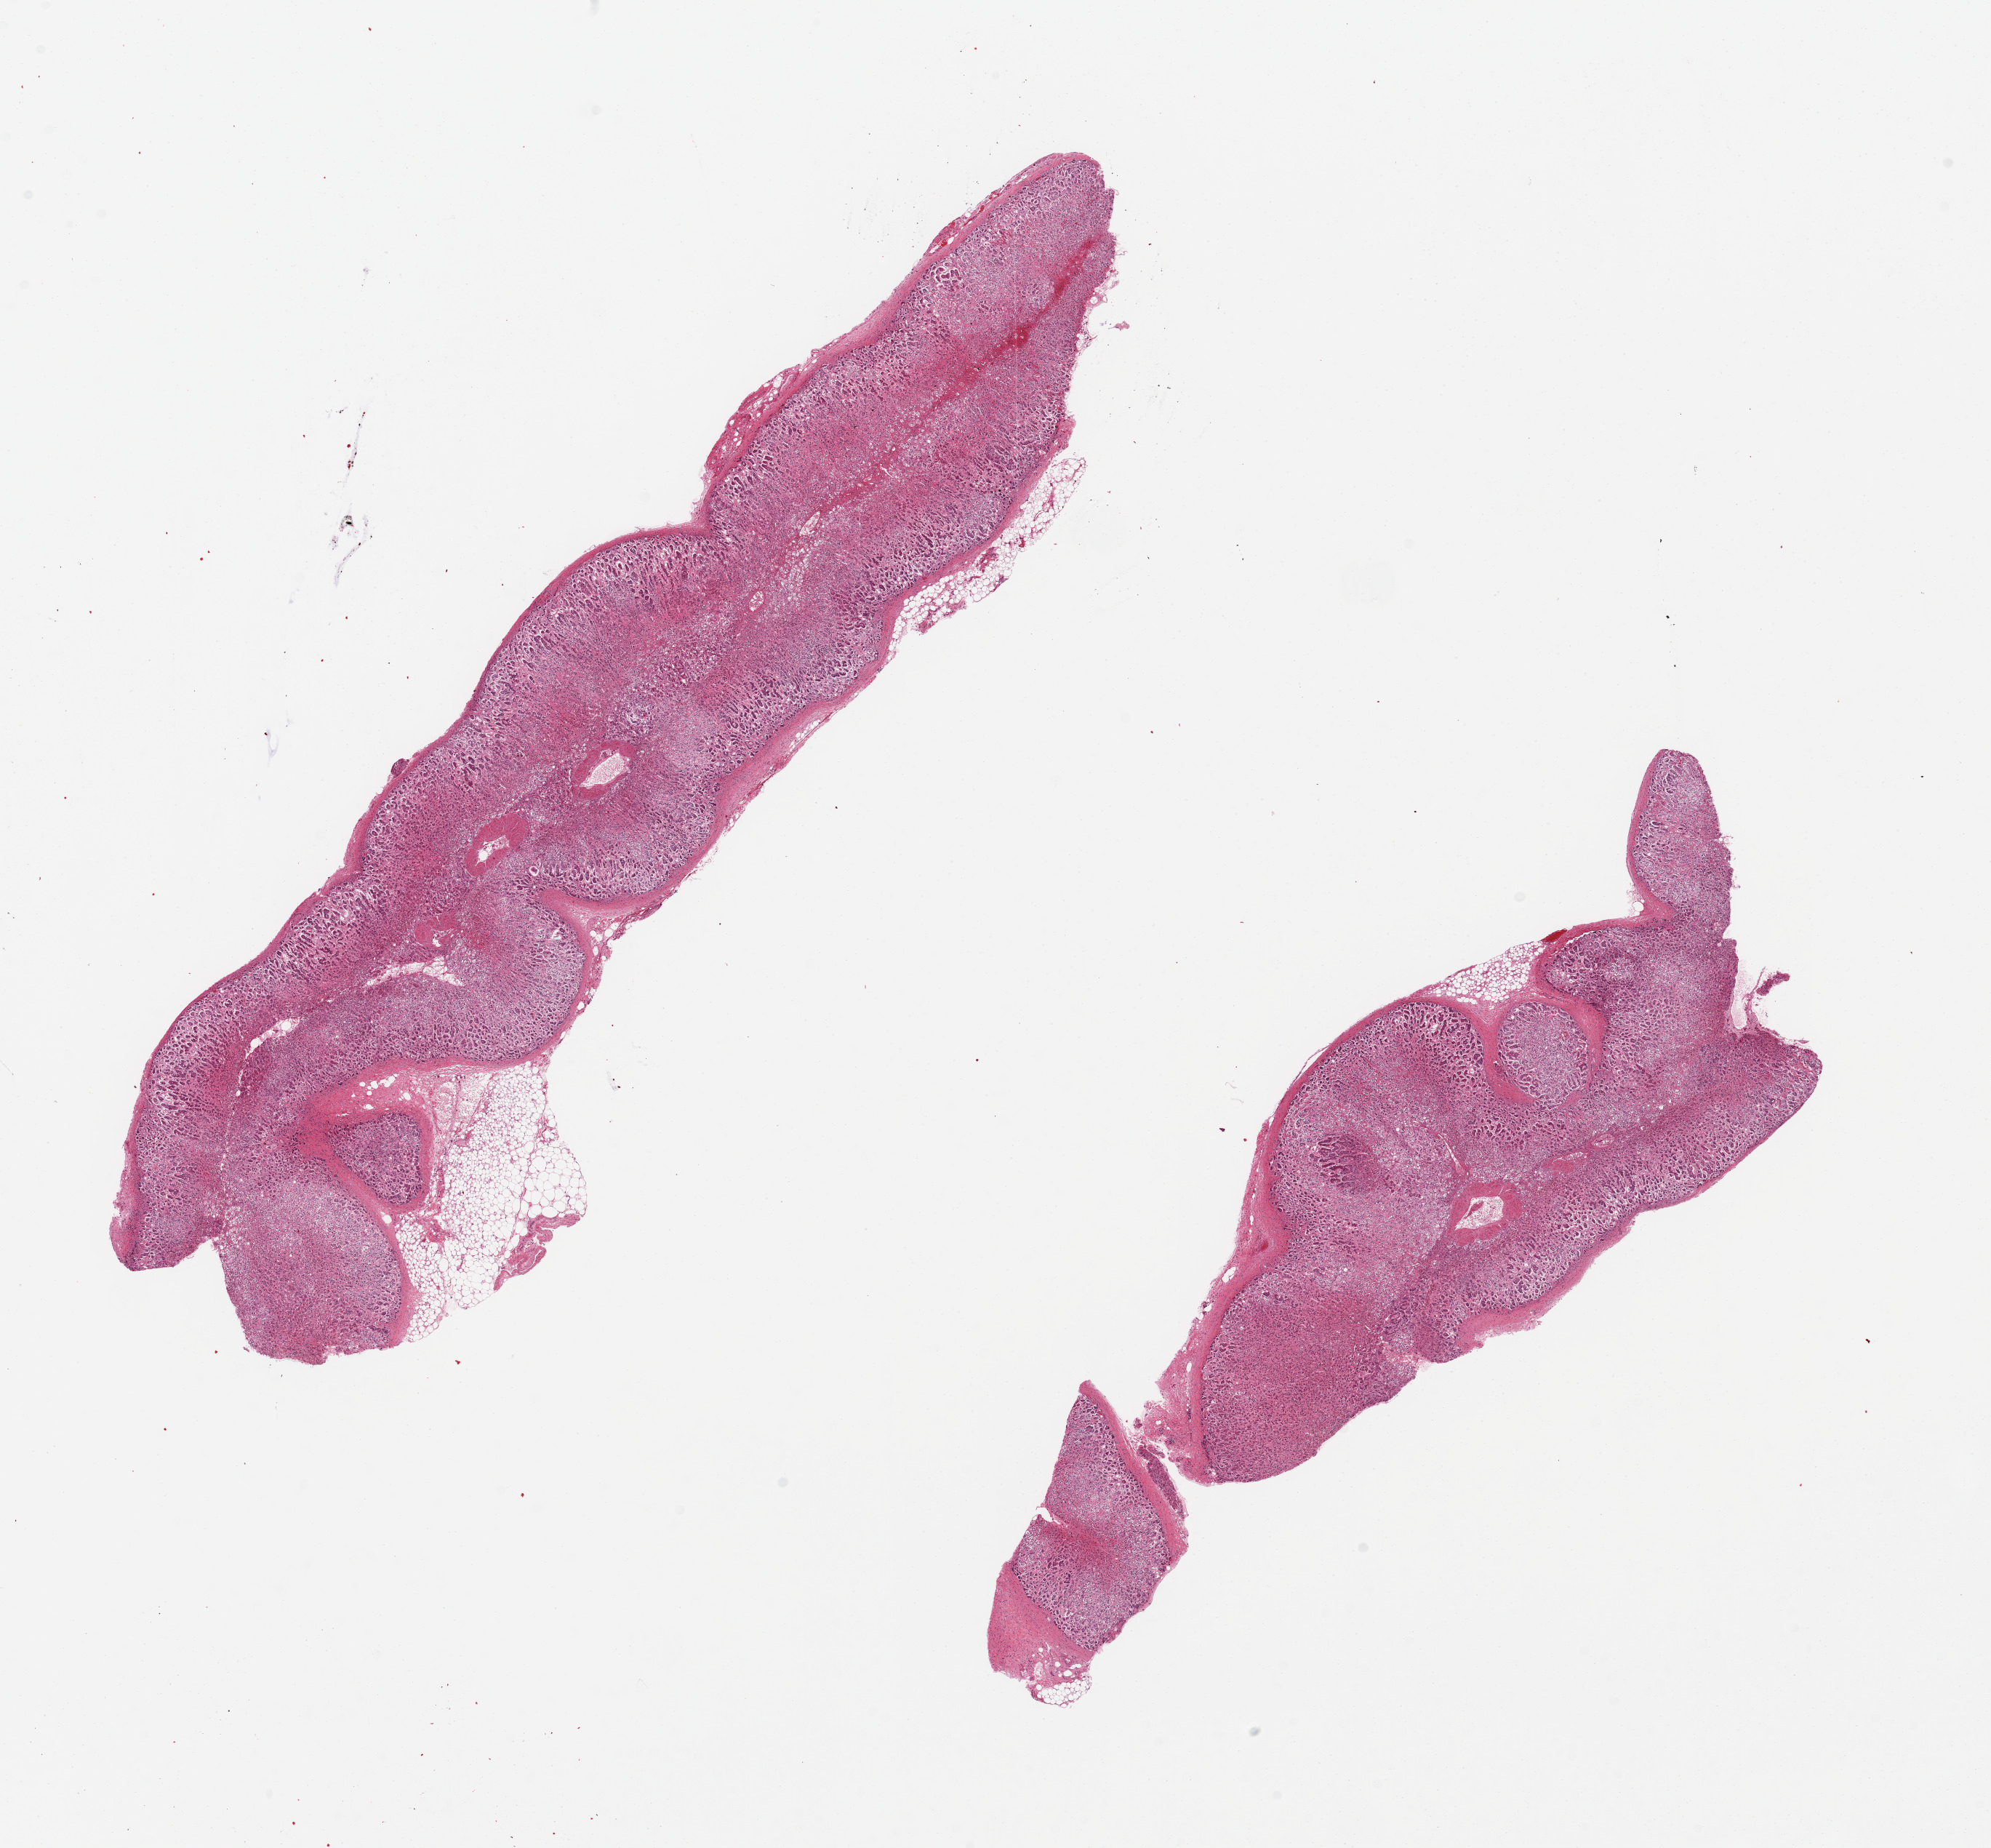
Digitized haematoxylin and eosin-stained section, low-resolution overview of the scanned area, about 21.7 x 20.1 mm (from a 20x scan). PAXgene-fixed, paraffin-embedded tissue. Target tissue: adrenal gland. Donor tissue sample.
Review note (as recorded): 2 pieces, all cortex, markdely autolyzed.